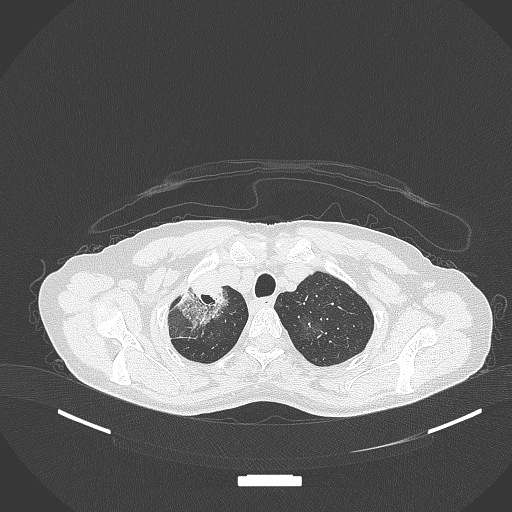
Chest CT, one axial slice. Position 282 of 284 along the scan axis. Reconstruction kernel B70f. 120 kVp. Lung window (W 1500 / L -600 HU). 512 × 512 image matrix, field of view 400 × 400 mm. Female patient, age 59 years. From the clinical record (not read from this slice): clinical TNM (as recorded): T3 N0 M0; histopathological grade: G1.
Annotated regions visible in this slice (rectangle marked by the reading radiologist):
- lung tumour (recorded histology: adenocarcinoma): bounding box [x1, y1, x2, y2] px = [174, 282, 224, 327]